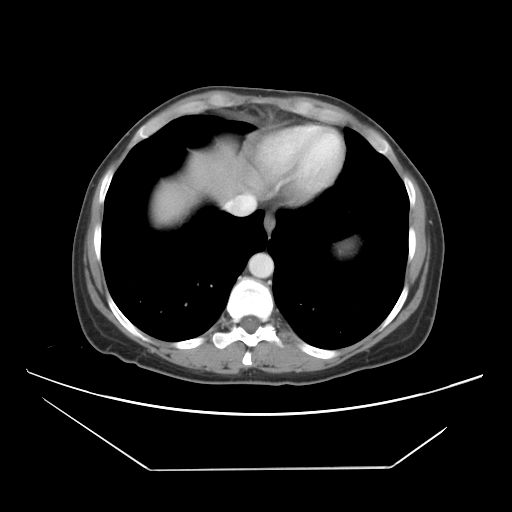
Contrast-enhanced abdominal CT, one axial slice. Slice 38 of 42 in the series (ordered by position). Intravenous contrast given. Soft-tissue window (W 400 / L 40 HU). 5 mm slice thickness. 512 × 512 image matrix, field of view 399 × 399 mm. Female patient, age 52 years. From the clinical record (not read from this slice): diagnosis: colorectal cancer liver metastases, imaged before liver resection; multiple liver metastases: yes; largest metastasis: 5.5 cm.
Outlined on this slice (expert manual segmentation):
- hepatic veins: box from (x=226, y=137) to (x=288, y=215) px